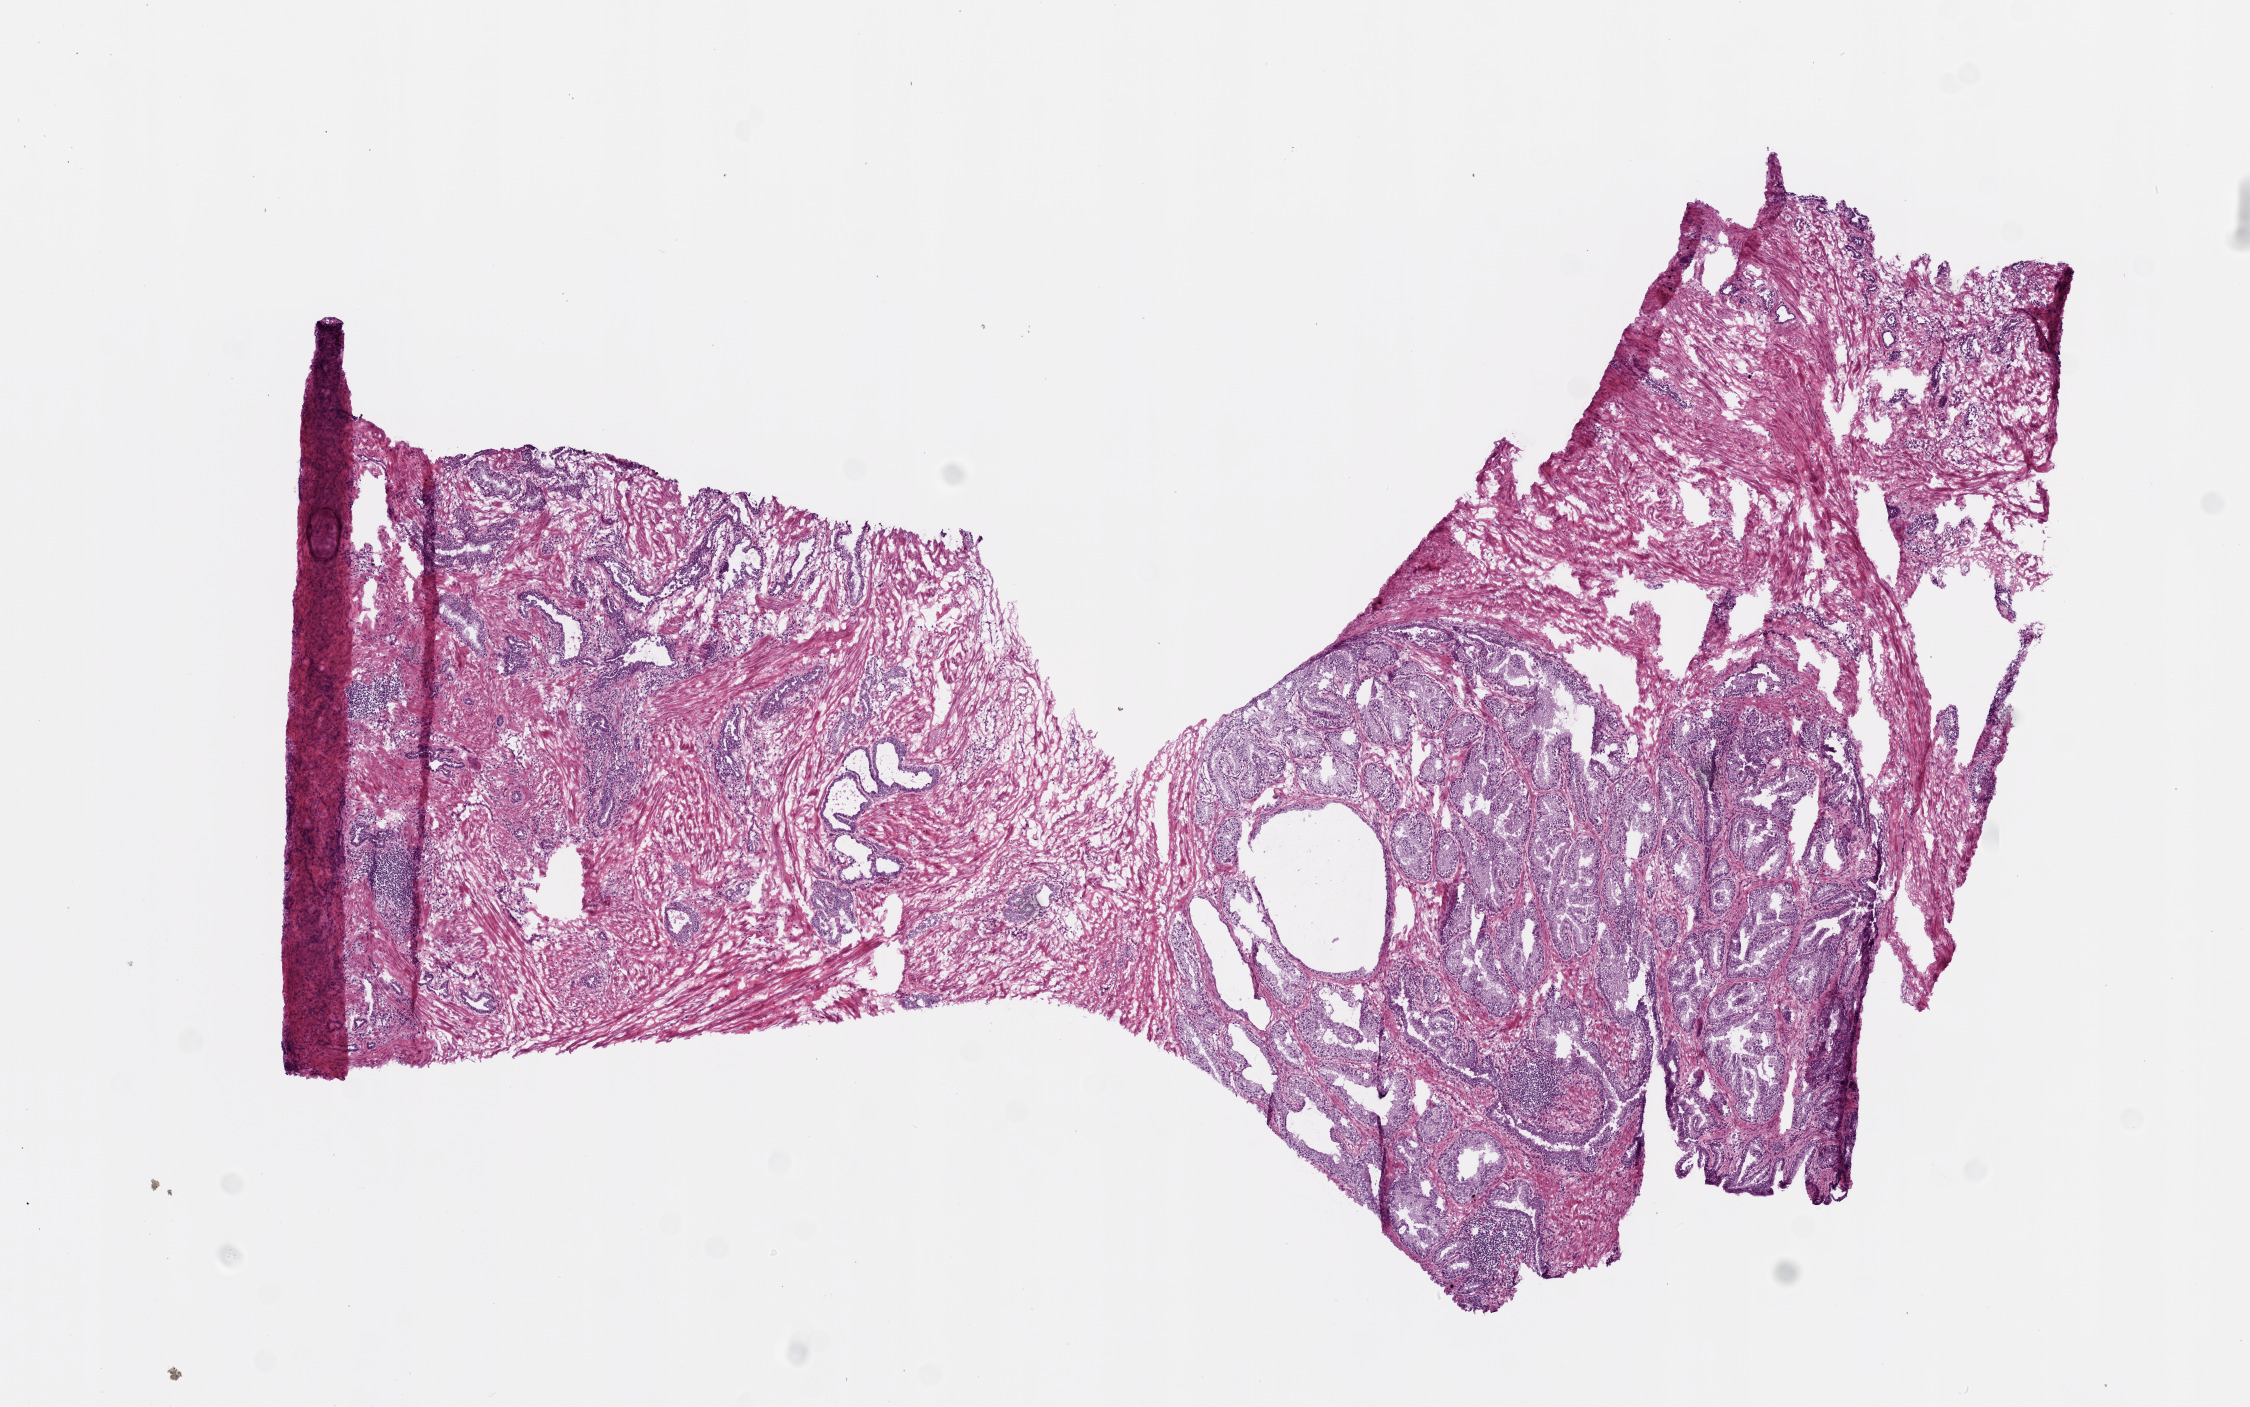
Digitized H&E tissue section (whole slide) — shown as a low-resolution overview of the whole scanned area (about 9.0 x 5.6 mm). Frozen section from the top of the tissue portion. Sample: solid tissue normal (non-tumour tissue), prostate. Patient: male, age at initial diagnosis 63 years.
- this section: solid tissue normal (non-tumour) sample from the same patient
- patient diagnosis: Acinar cell carcinoma